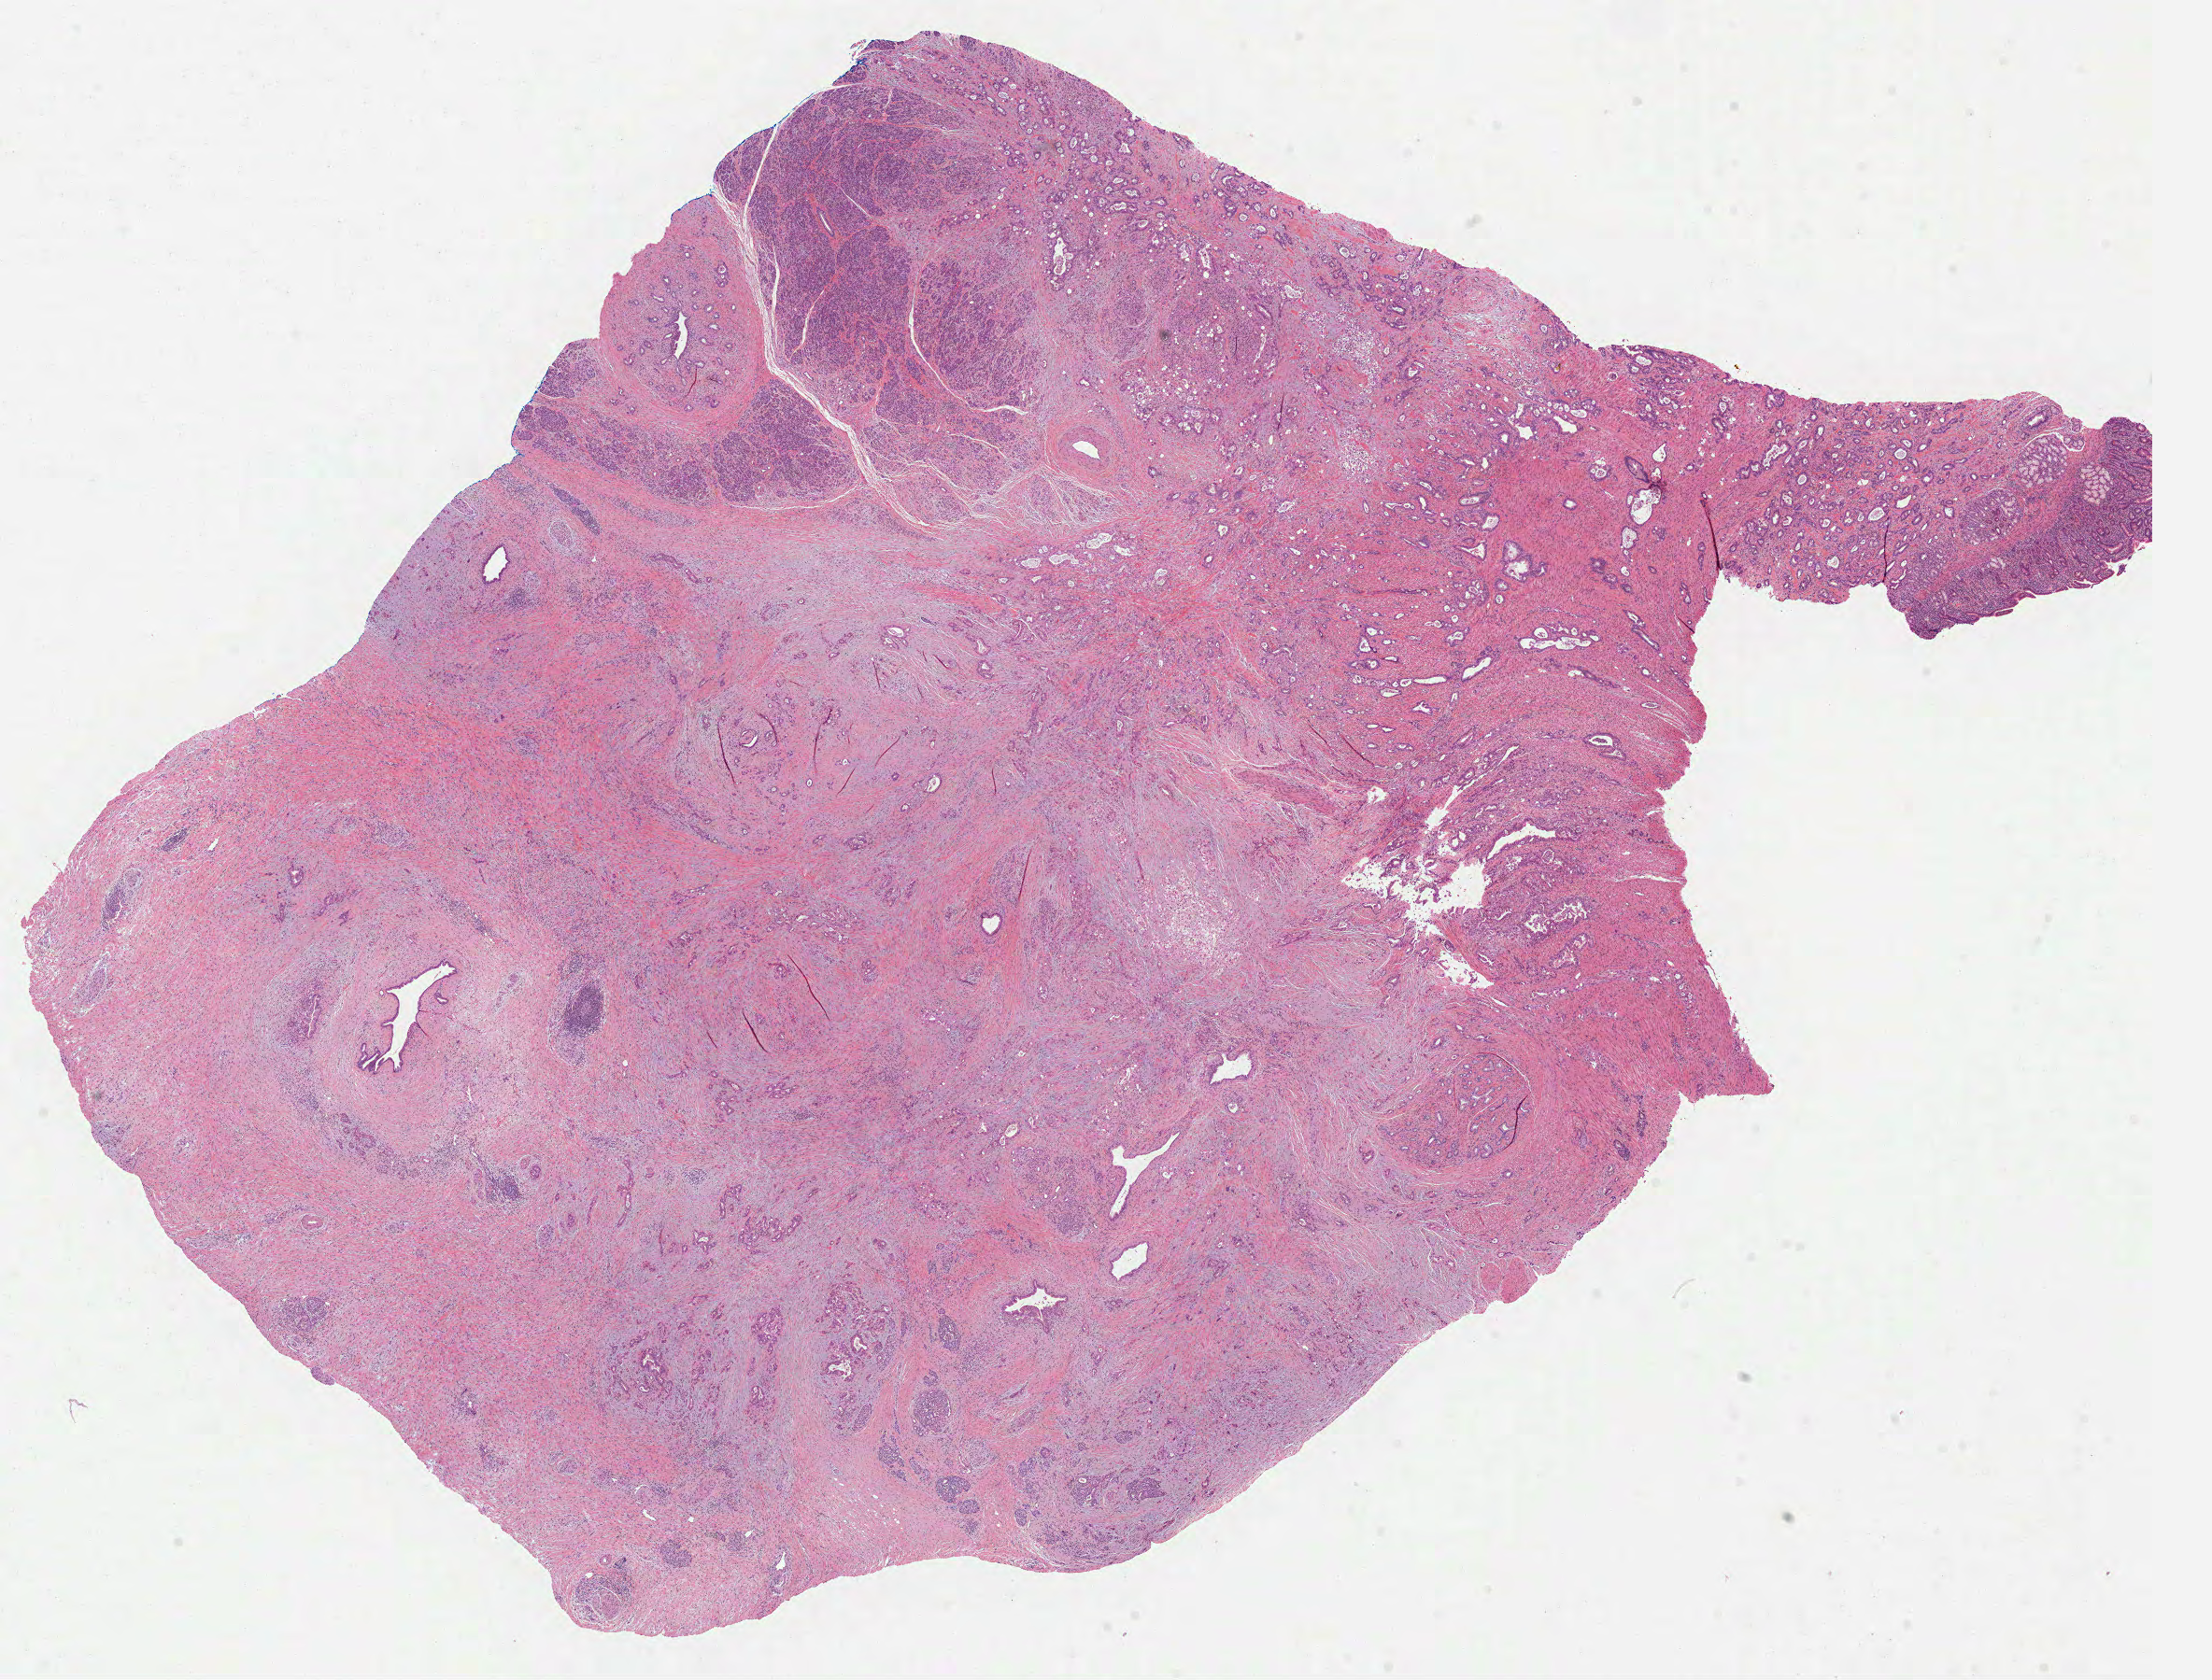
Whole-slide histology image, Hematoxylin and eosin (H&E) stained — whole scanned area (about 19.1 x 14.5 mm, from a 40x scan) shown as a low-resolution overview; FFPE section; pancreas, primary tumour sample. Patient: female, age at initial diagnosis 61 years. Histologic grade: G1 (well differentiated).
• lymph nodes positive (case pathology): 3 of 15 examined
• AJCC pathologic stage: IIB
• pathologic diagnosis: Infiltrating duct carcinoma, NOS (head of pancreas)